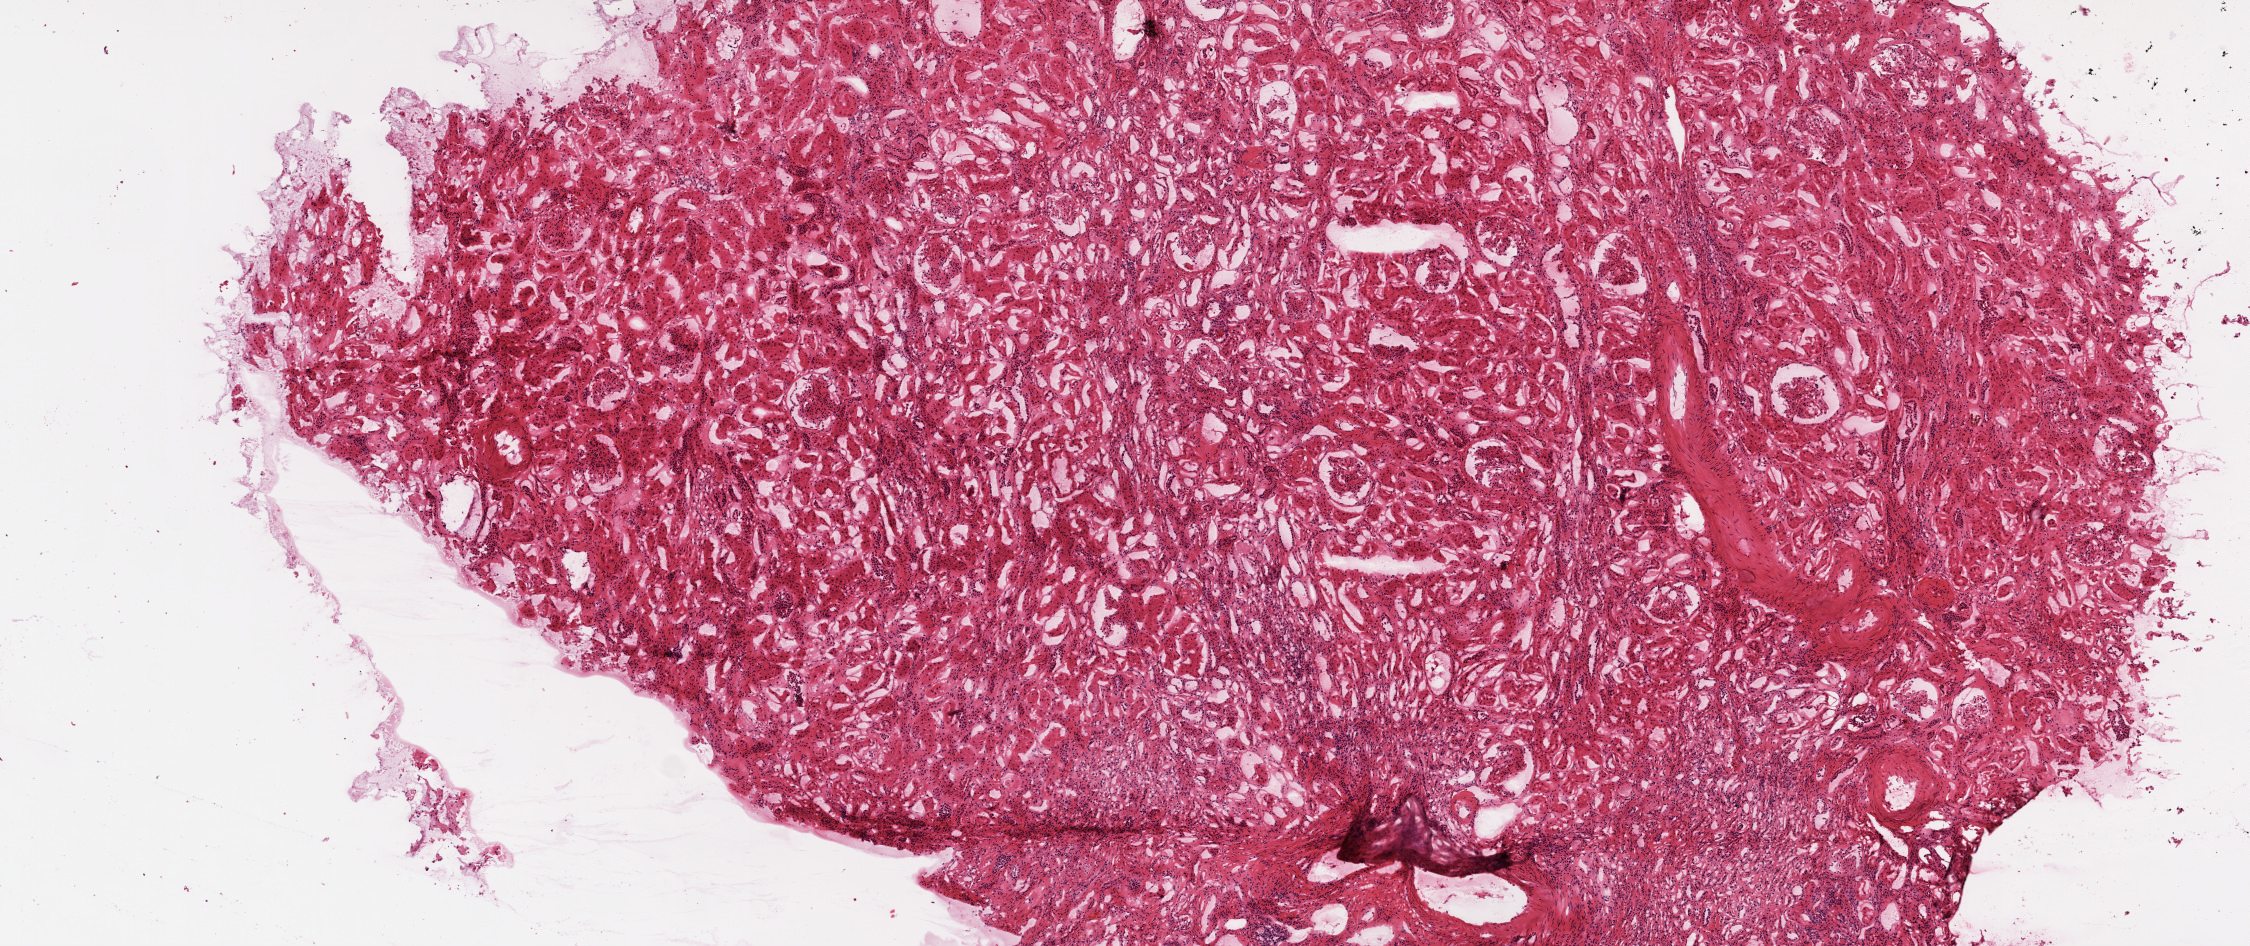
Digitized H&E tissue section (whole slide), whole scanned area (about 9.0 x 3.8 mm) shown as a low-resolution overview; frozen section from the top of the tissue portion; solid tissue normal (non-tumour tissue) sample from the kidney. Male, age 72 years at initial diagnosis.
This section: solid tissue normal (non-tumour) sample from the same patient. Patient diagnosis: Clear cell adenocarcinoma, NOS.